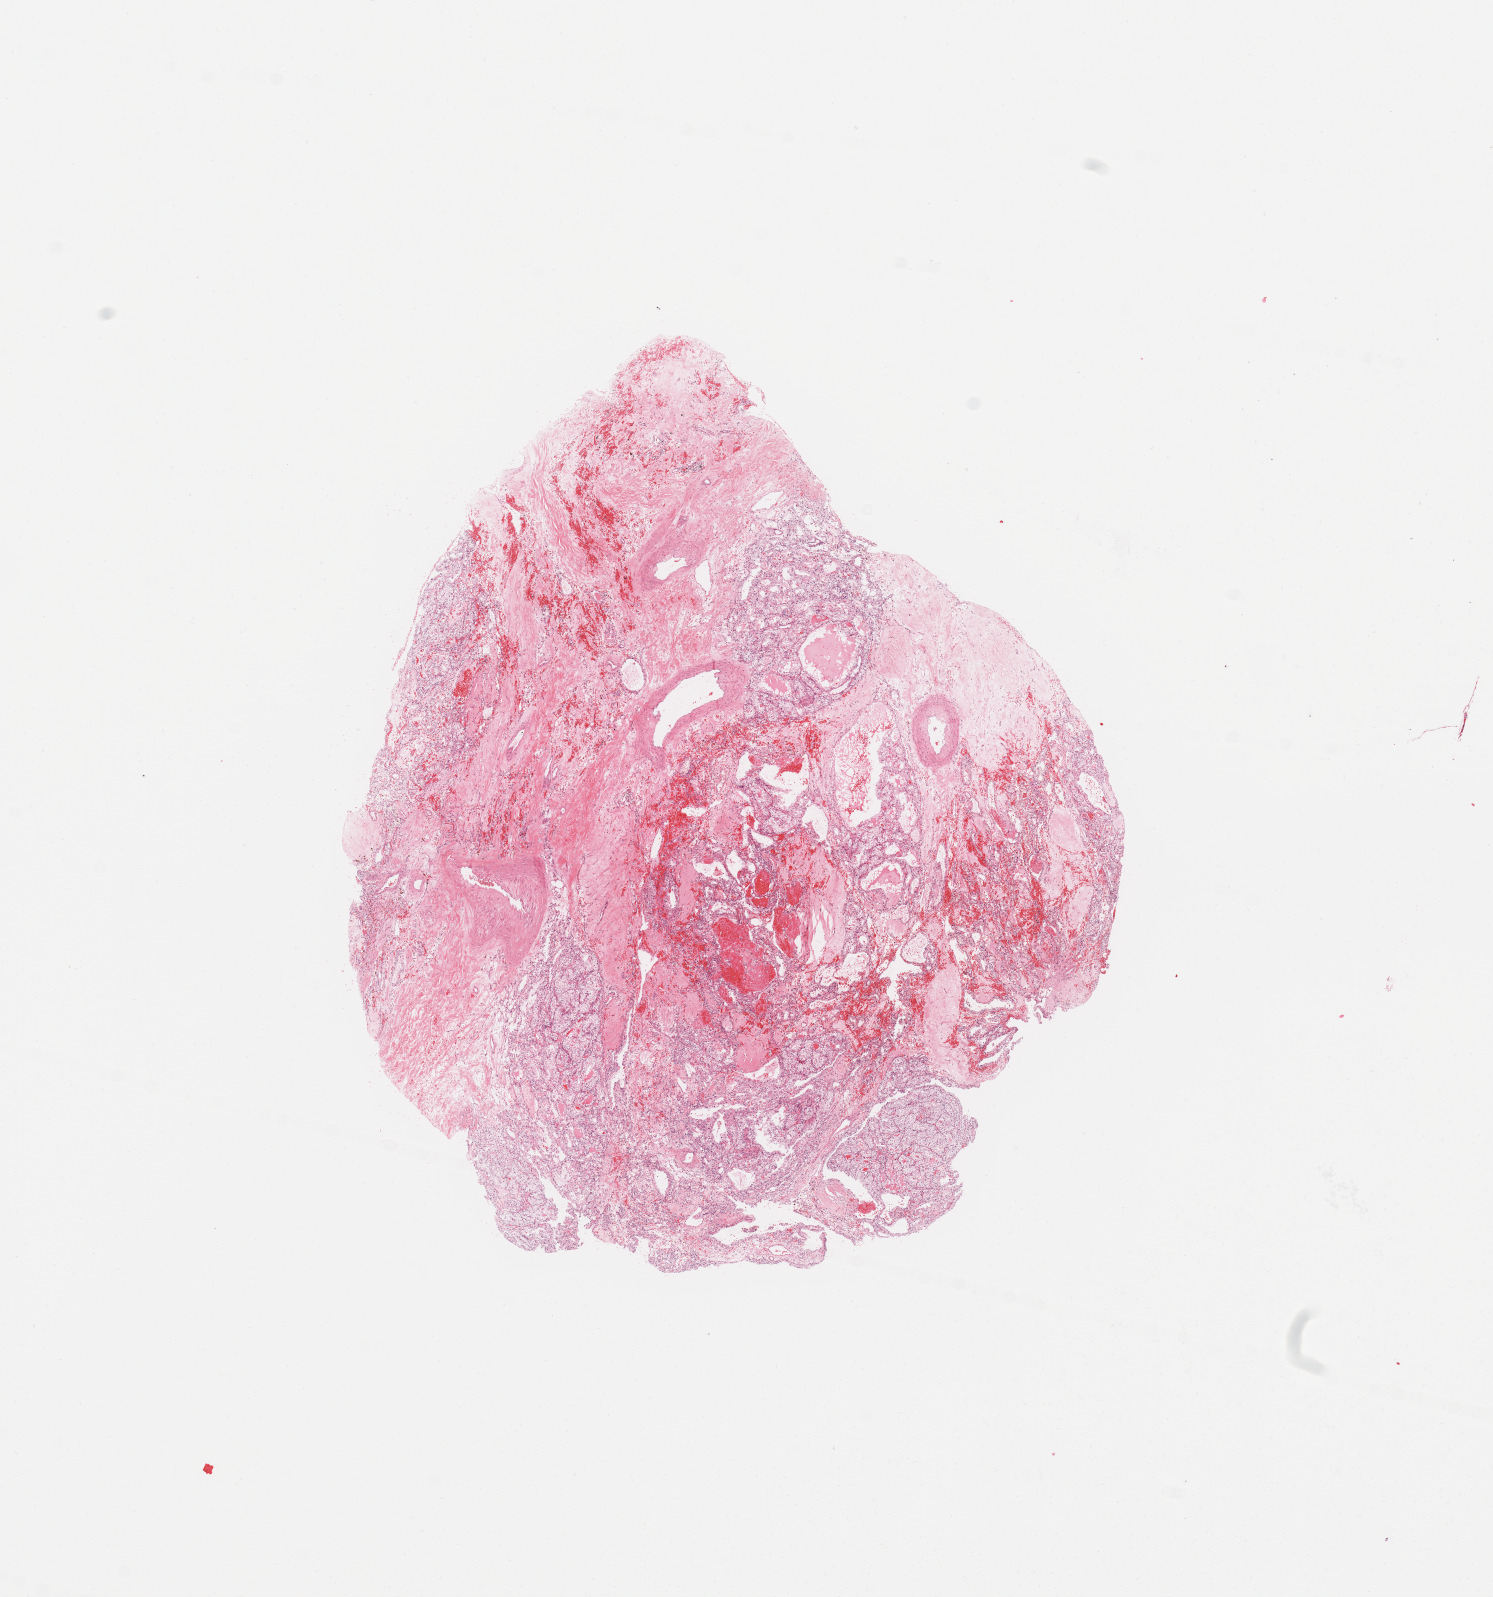
Digitized Hematoxylin and eosin (H&E) stained tissue section (whole slide), a low-resolution overview of the entire scanned area, about 11.8 x 12.6 mm (from a 20x scan), tumour tissue sample, sampled site: kidney. Male, 31 y/o. Histologic grade: G2 (moderately differentiated). Slide review estimates, as recorded: tumour nuclei 80%, necrosis 5%.
Primary tumour site (as recorded): lower pole. Diagnosis: Renal cell carcinoma, NOS. AJCC pathologic stage: I.